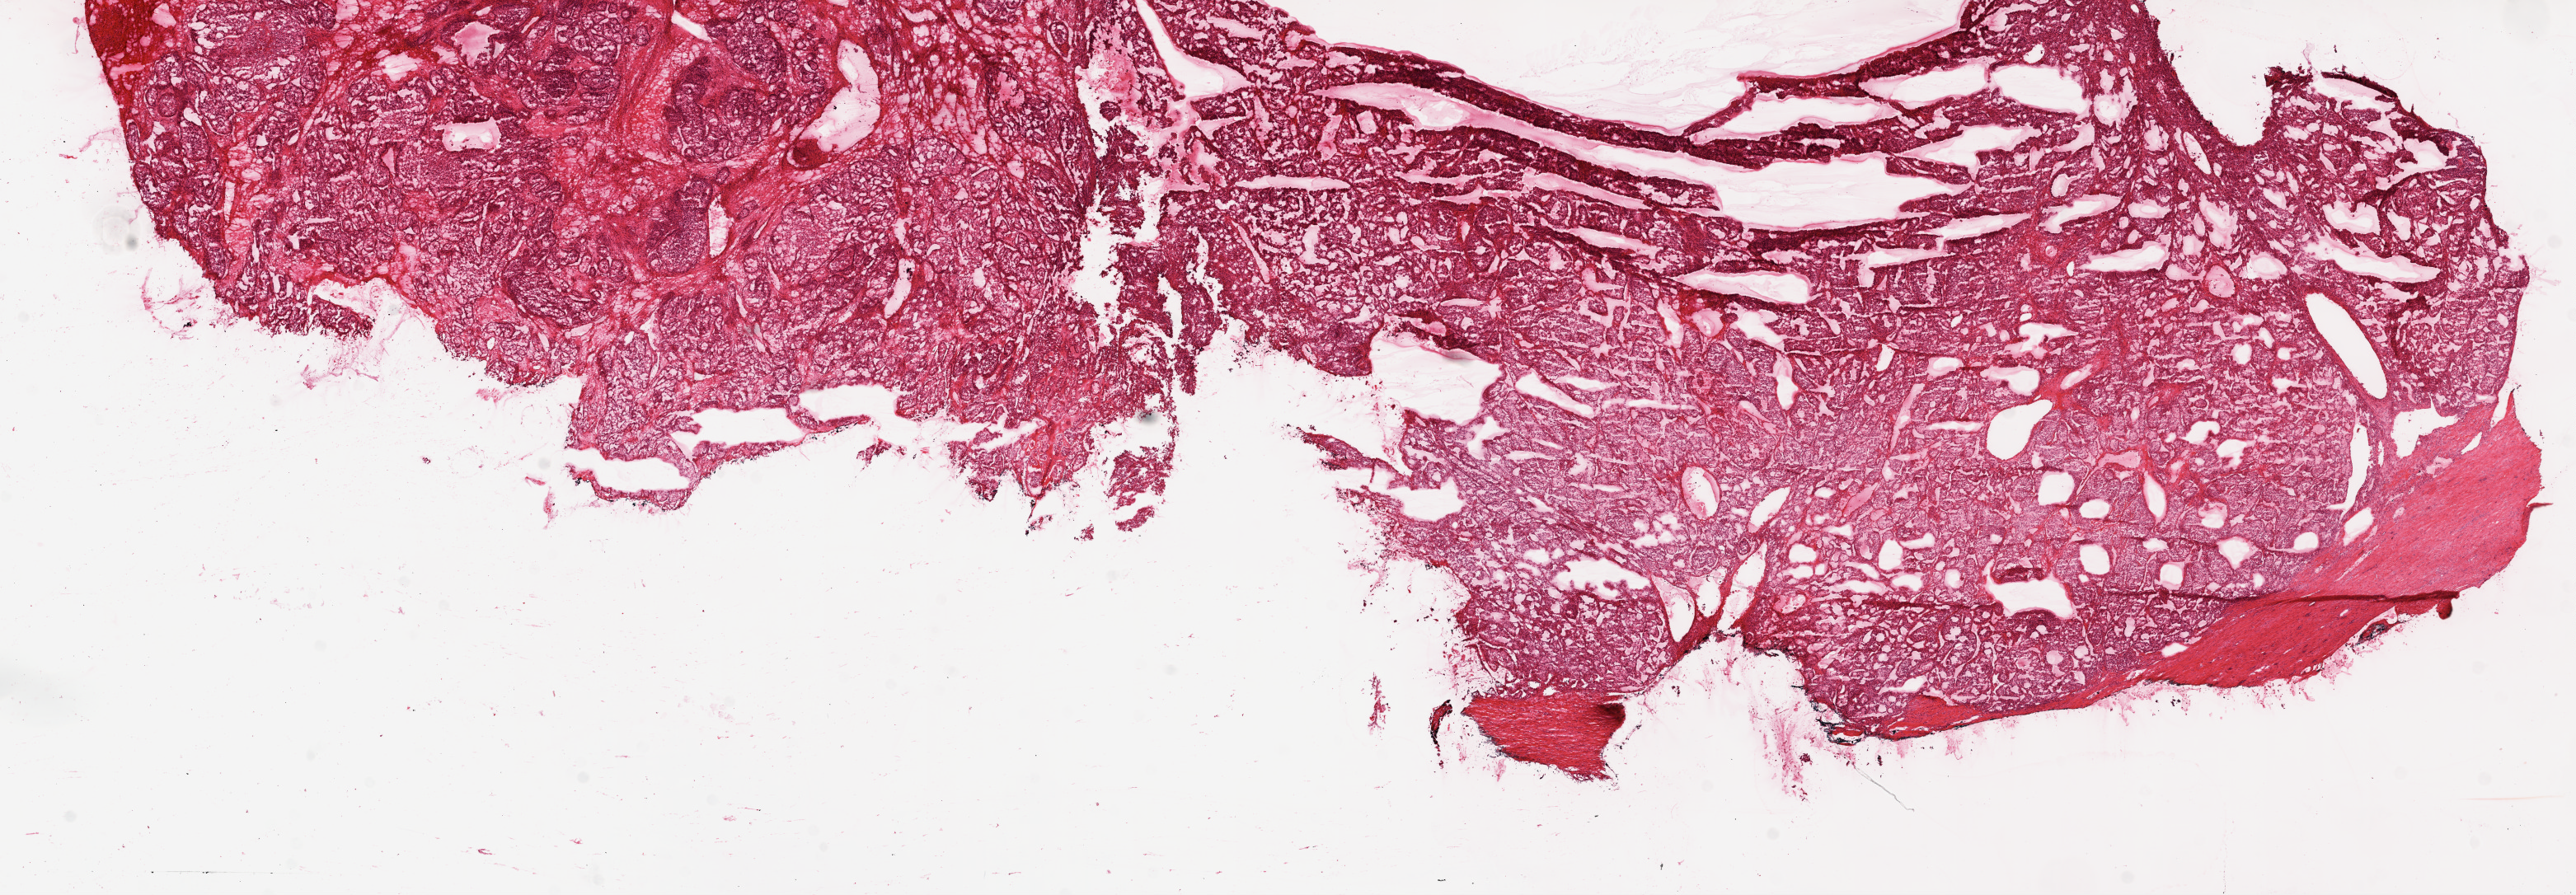
H&E-stained whole-slide image — shown as a low-resolution overview of the whole scanned area (about 25.1 x 8.7 mm, acquisition: 20x scan); frozen section; sample: primary tumour, kidney. Patient: male, age at initial diagnosis 68 years. Histologic grade: G3 (poorly differentiated). Pathologist review of this section (percent, as recorded): tumour cells 80%, tumour nuclei 80%, normal cells 0%, stromal cells 20%, necrosis 0%.
Diagnosis: Clear cell adenocarcinoma, NOS. TNM: T3b NX M0. AJCC pathologic stage: III.